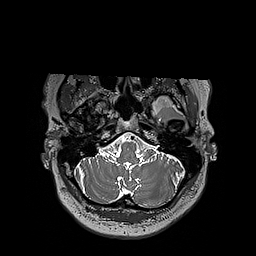
Brain MRI from a brain-tumour surgery series, one axial slice. Slice 158 of 192 in the series (ordered by position). 256 × 256 image matrix, field of view 250 × 250 mm. Case-level facts recorded for this patient, not image findings: histopathology: Oligodendroglioma; WHO grade: 3.
Outlined on this slice (manually delineated by an expert):
- tumour: box from (x=124, y=94) to (x=197, y=111) px